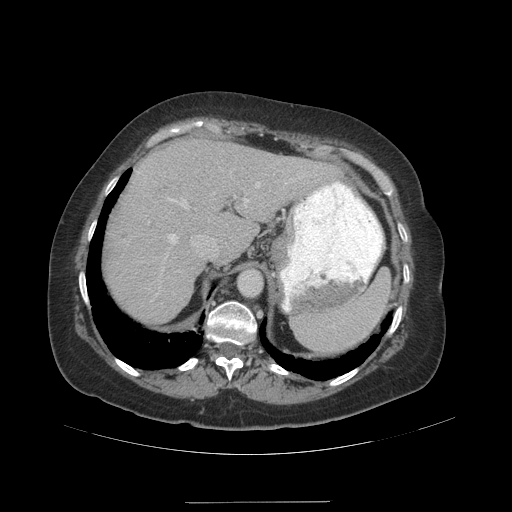
Contrast-enhanced abdominal CT (liver protocol), one axial slice; position 74 of 99 along the scan axis; reconstruction kernel STANDARD; 140 kVp; soft-tissue window (W 400 / L 40 HU); 2.5 mm slice thickness; 512 × 512 image matrix, field of view 440 × 440 mm. Case-level facts recorded for this patient, not image findings: diagnosis: hepatocellular carcinoma (patient treated with transarterial chemoembolisation; whether this scan precedes or follows treatment is not stated here); TNM stage (as recorded): Stage-IVA; Child-Pugh class: A; tumour nodularity: multinodular.
Outlined on this slice (semi-automatically segmented with operator editing):
- abdominal aorta: box from (x=237, y=269) to (x=261, y=297) px
- liver parenchyma outside the tumour (the mass and vessels are separate outlines, so this box may not span the whole liver): (x=104, y=138)–(x=338, y=322)
- mass: (x=119, y=227)–(x=128, y=238)
- liver vessels: (x=163, y=176)–(x=301, y=270)